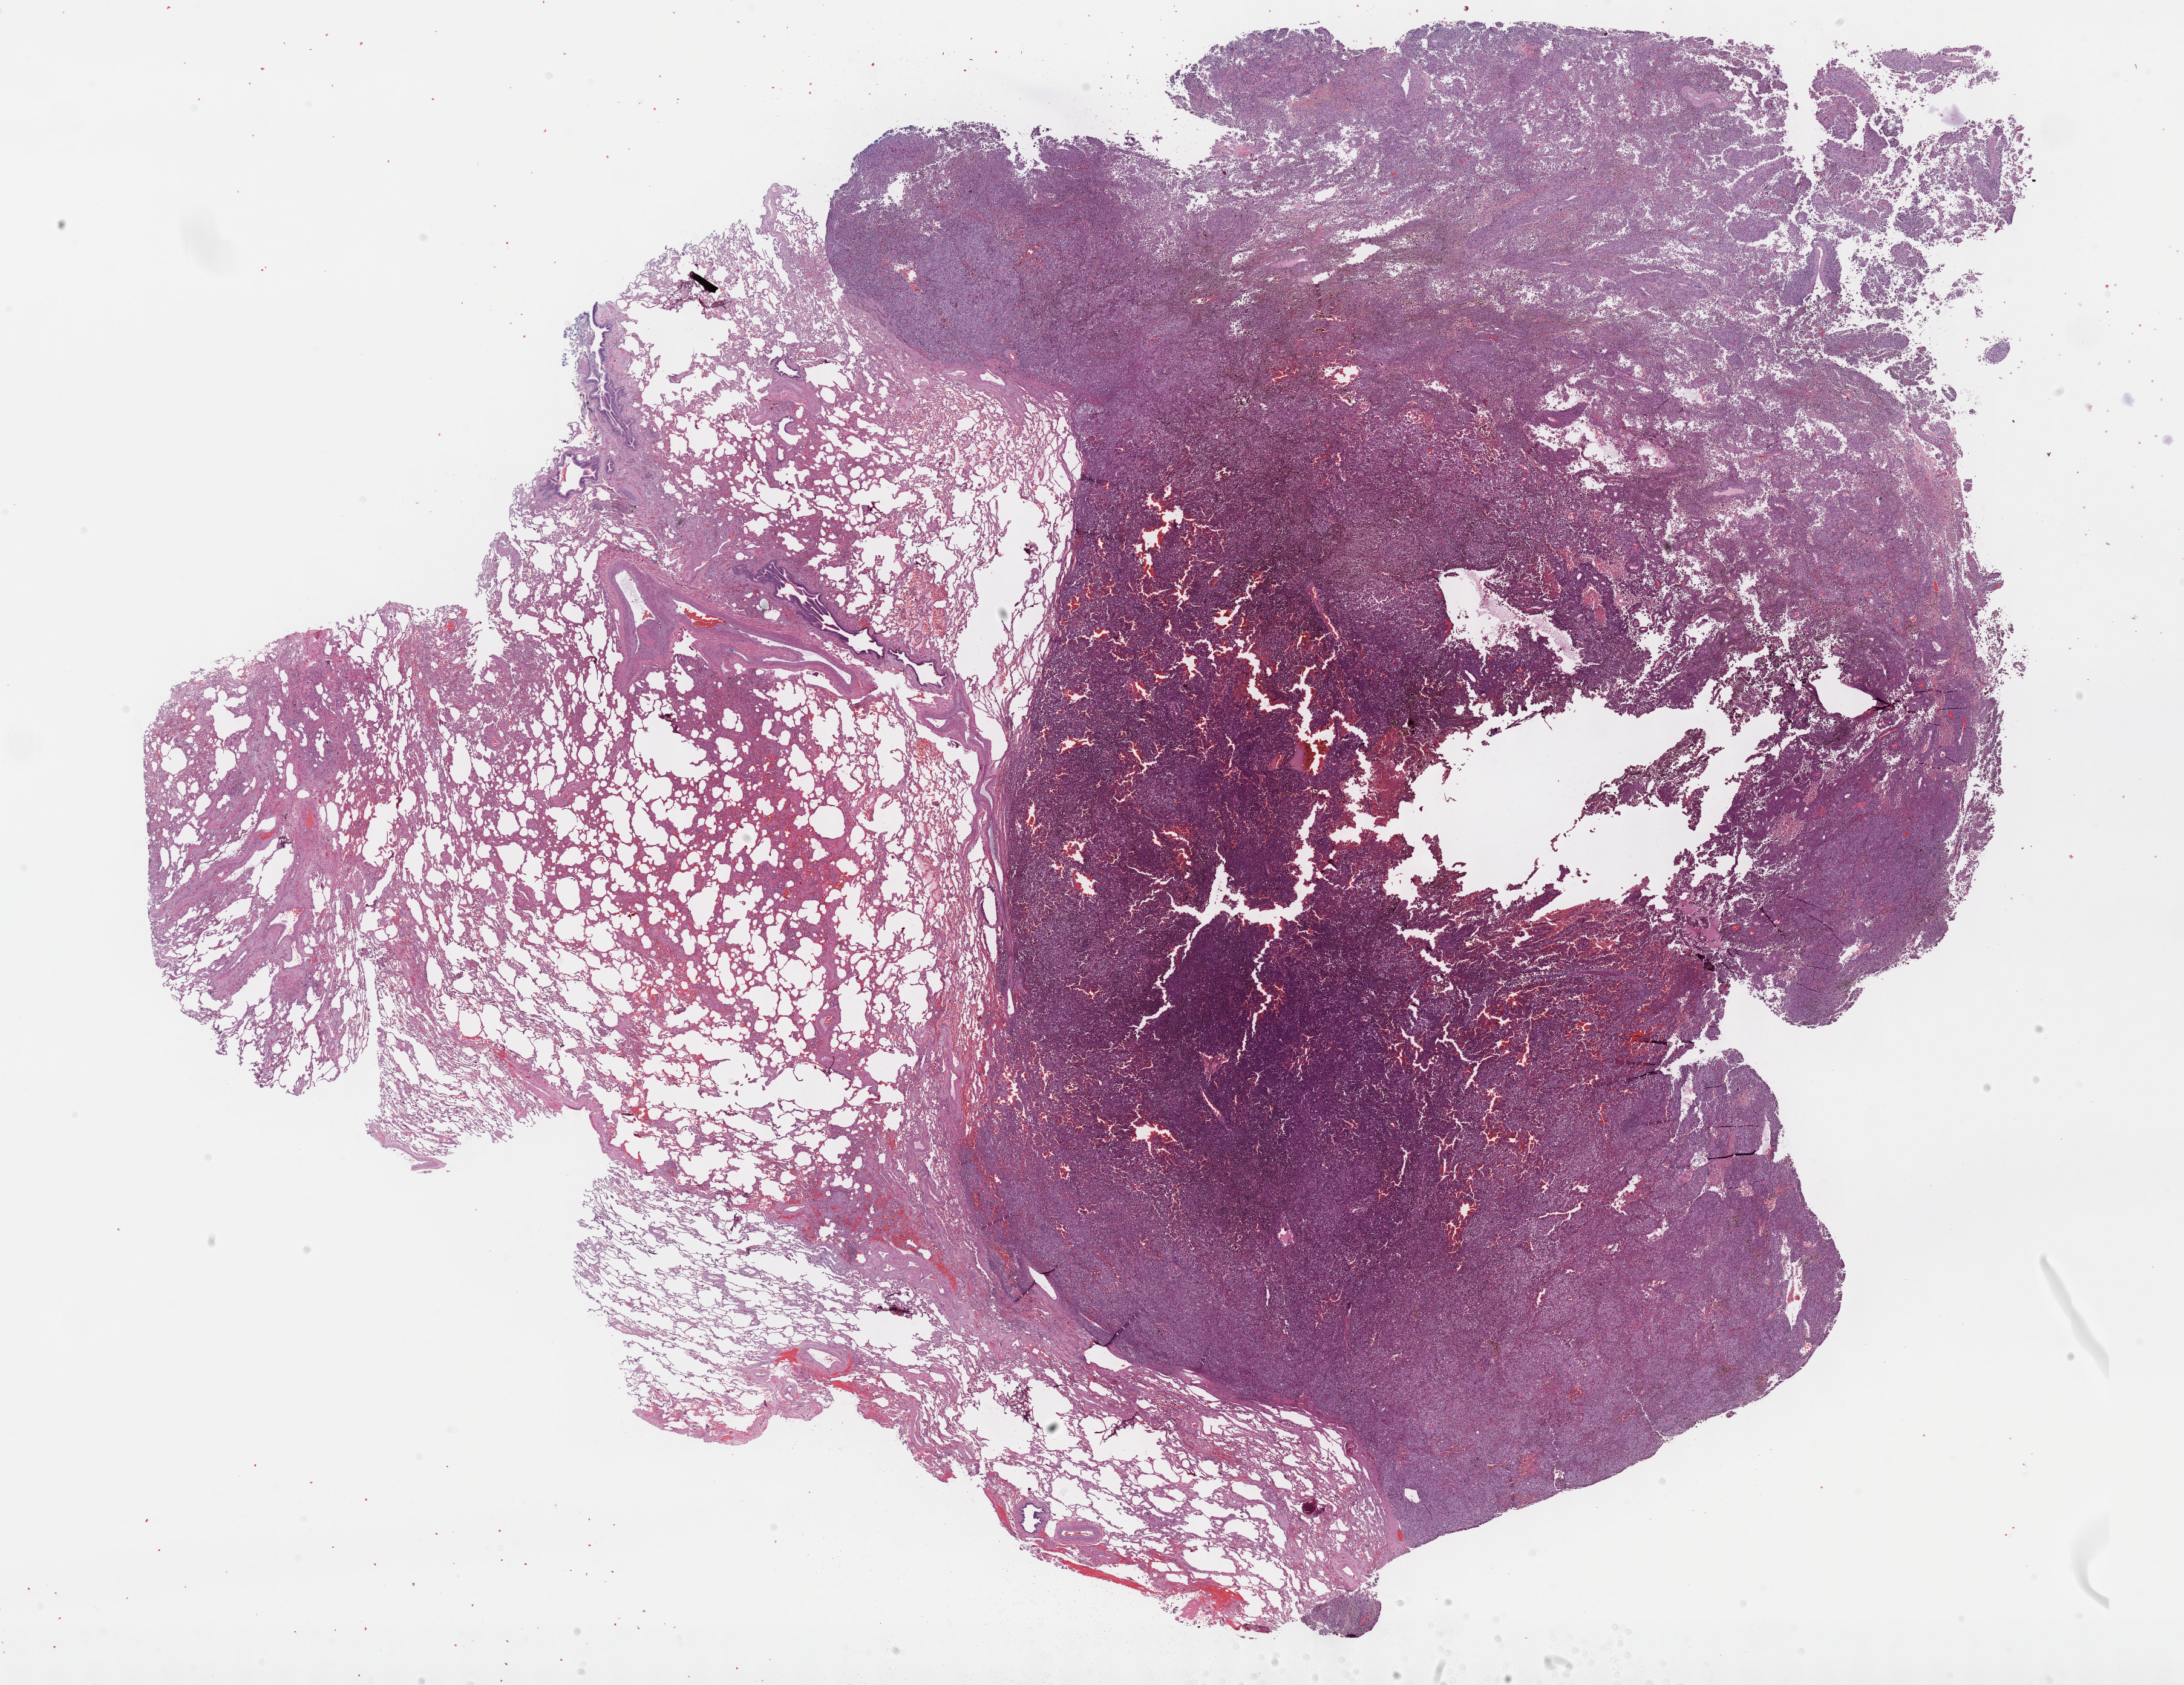
Hematoxylin and eosin (H&E) stained whole-slide image — a low-resolution overview of the entire scanned area, about 29.2 x 22.5 mm (from a 40x scan), formalin-fixed paraffin-embedded (FFPE) diagnostic section, metastatic tumour sample, sampled site not recorded. Male, age 70 years at initial diagnosis.
This section: metastatic tumour tissue. Patient diagnosis: Malignant melanoma, NOS.